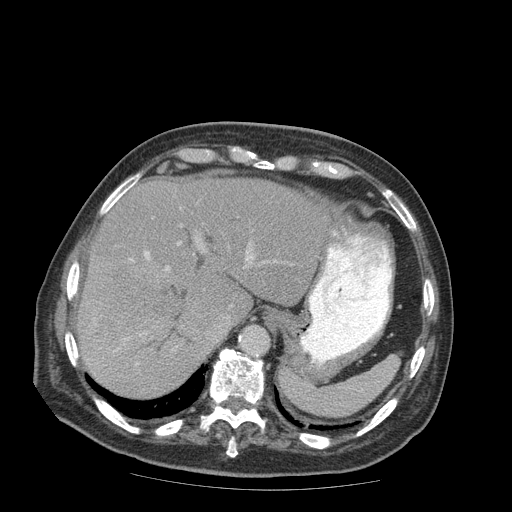
Contrast-enhanced abdominal CT (liver protocol), one axial slice. Soft-tissue window (W 400 / L 40 HU). 512 × 512 image matrix, field of view 420 × 420 mm. Case-level facts recorded for this patient, not image findings: diagnosis: hepatocellular carcinoma (patient treated with transarterial chemoembolisation; whether this scan precedes or follows treatment is not stated here); TNM stage (as recorded): Stage-IIIB; Child-Pugh class: A; tumour nodularity: multinodular.
Annotated regions visible in this slice (semi-automatically segmented with operator editing):
- liver parenchyma outside the tumour (the mass and vessels are separate outlines, so this box may not span the whole liver): bounding box <78,178,332,398> (left, top, right, bottom; pixels)
- mass: <83,248,182,337>
- liver vessels: <114,239,254,365>